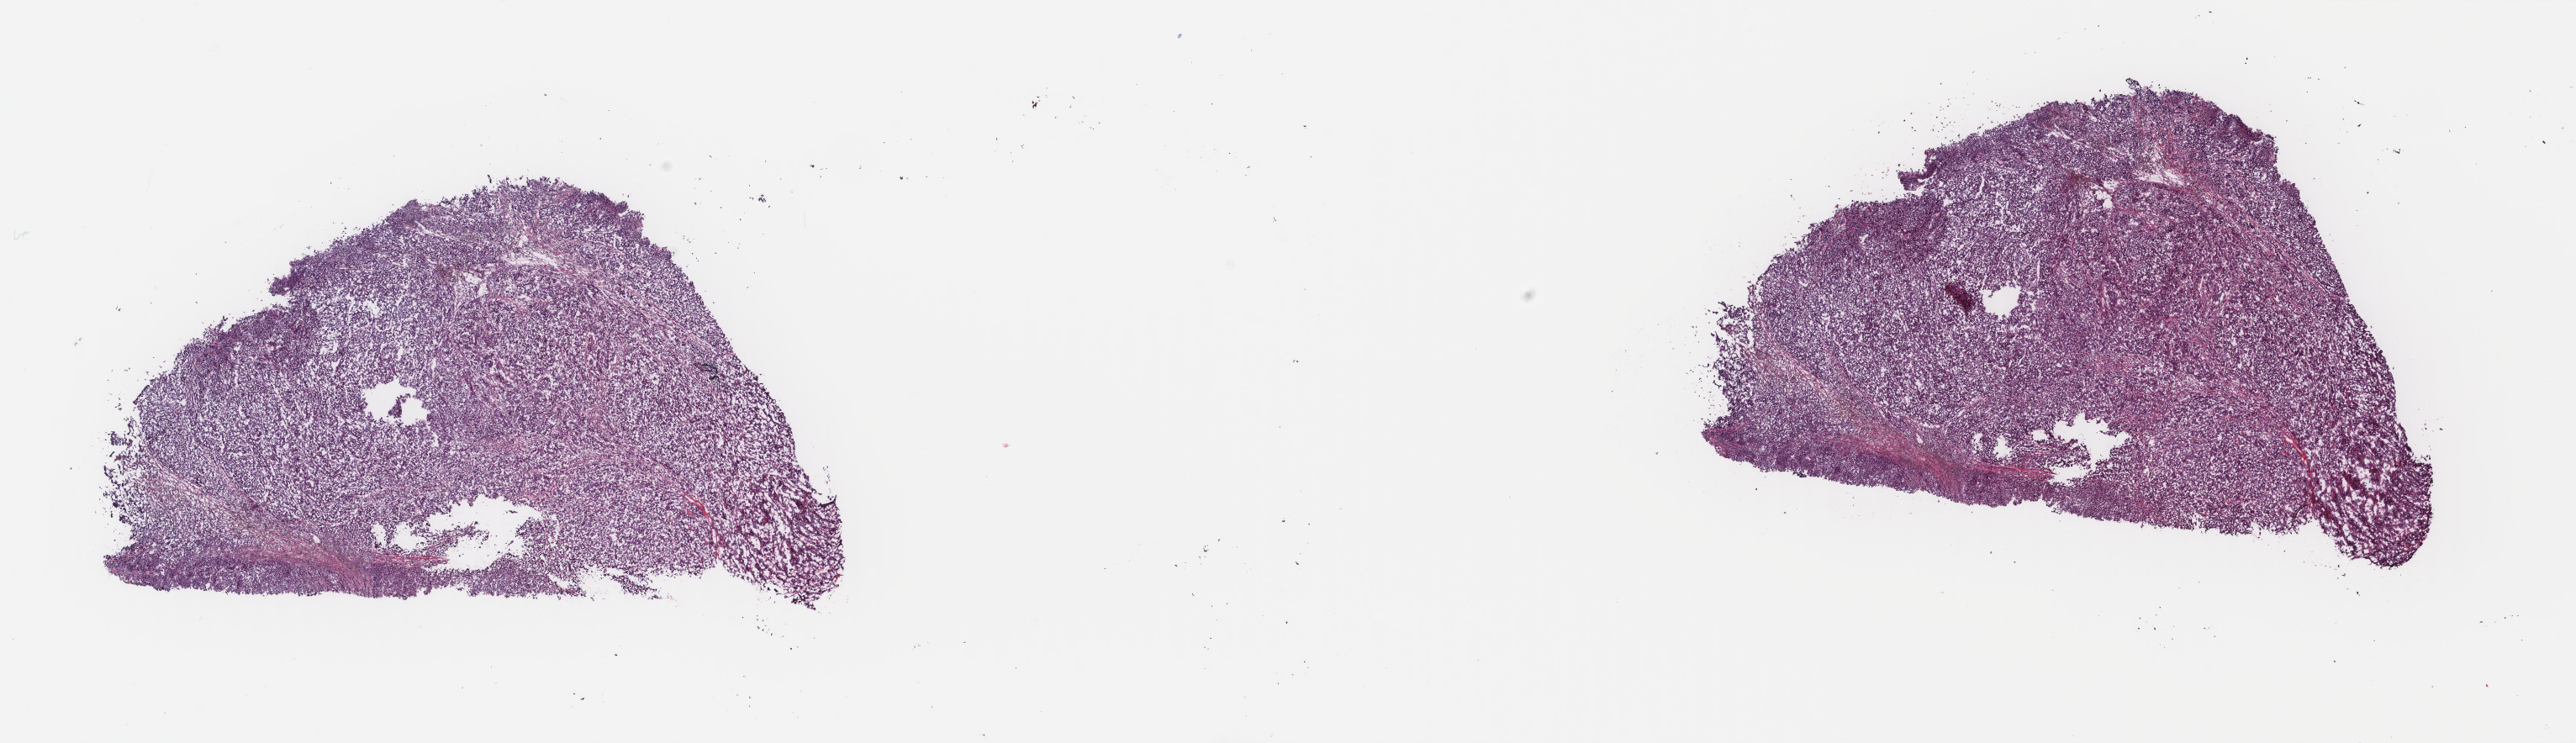
H&E-stained whole-slide image, whole scanned area (about 24.3 x 7.0 mm) shown as a low-resolution overview. Frozen section. Metastatic tumour sample, sampled site not recorded. Female, age 48 years at initial diagnosis. Pathologist review of this section (percent, as recorded): tumour cells 100%, tumour nuclei 90%, normal cells 0%, stromal cells 0%, necrosis 0%. Inflammatory infiltration, as recorded: lymphocyte infiltration 0%, monocyte infiltration 0%, neutrophil infiltration 0%.
* this section: metastatic tumour tissue
* patient diagnosis: Malignant melanoma, NOS